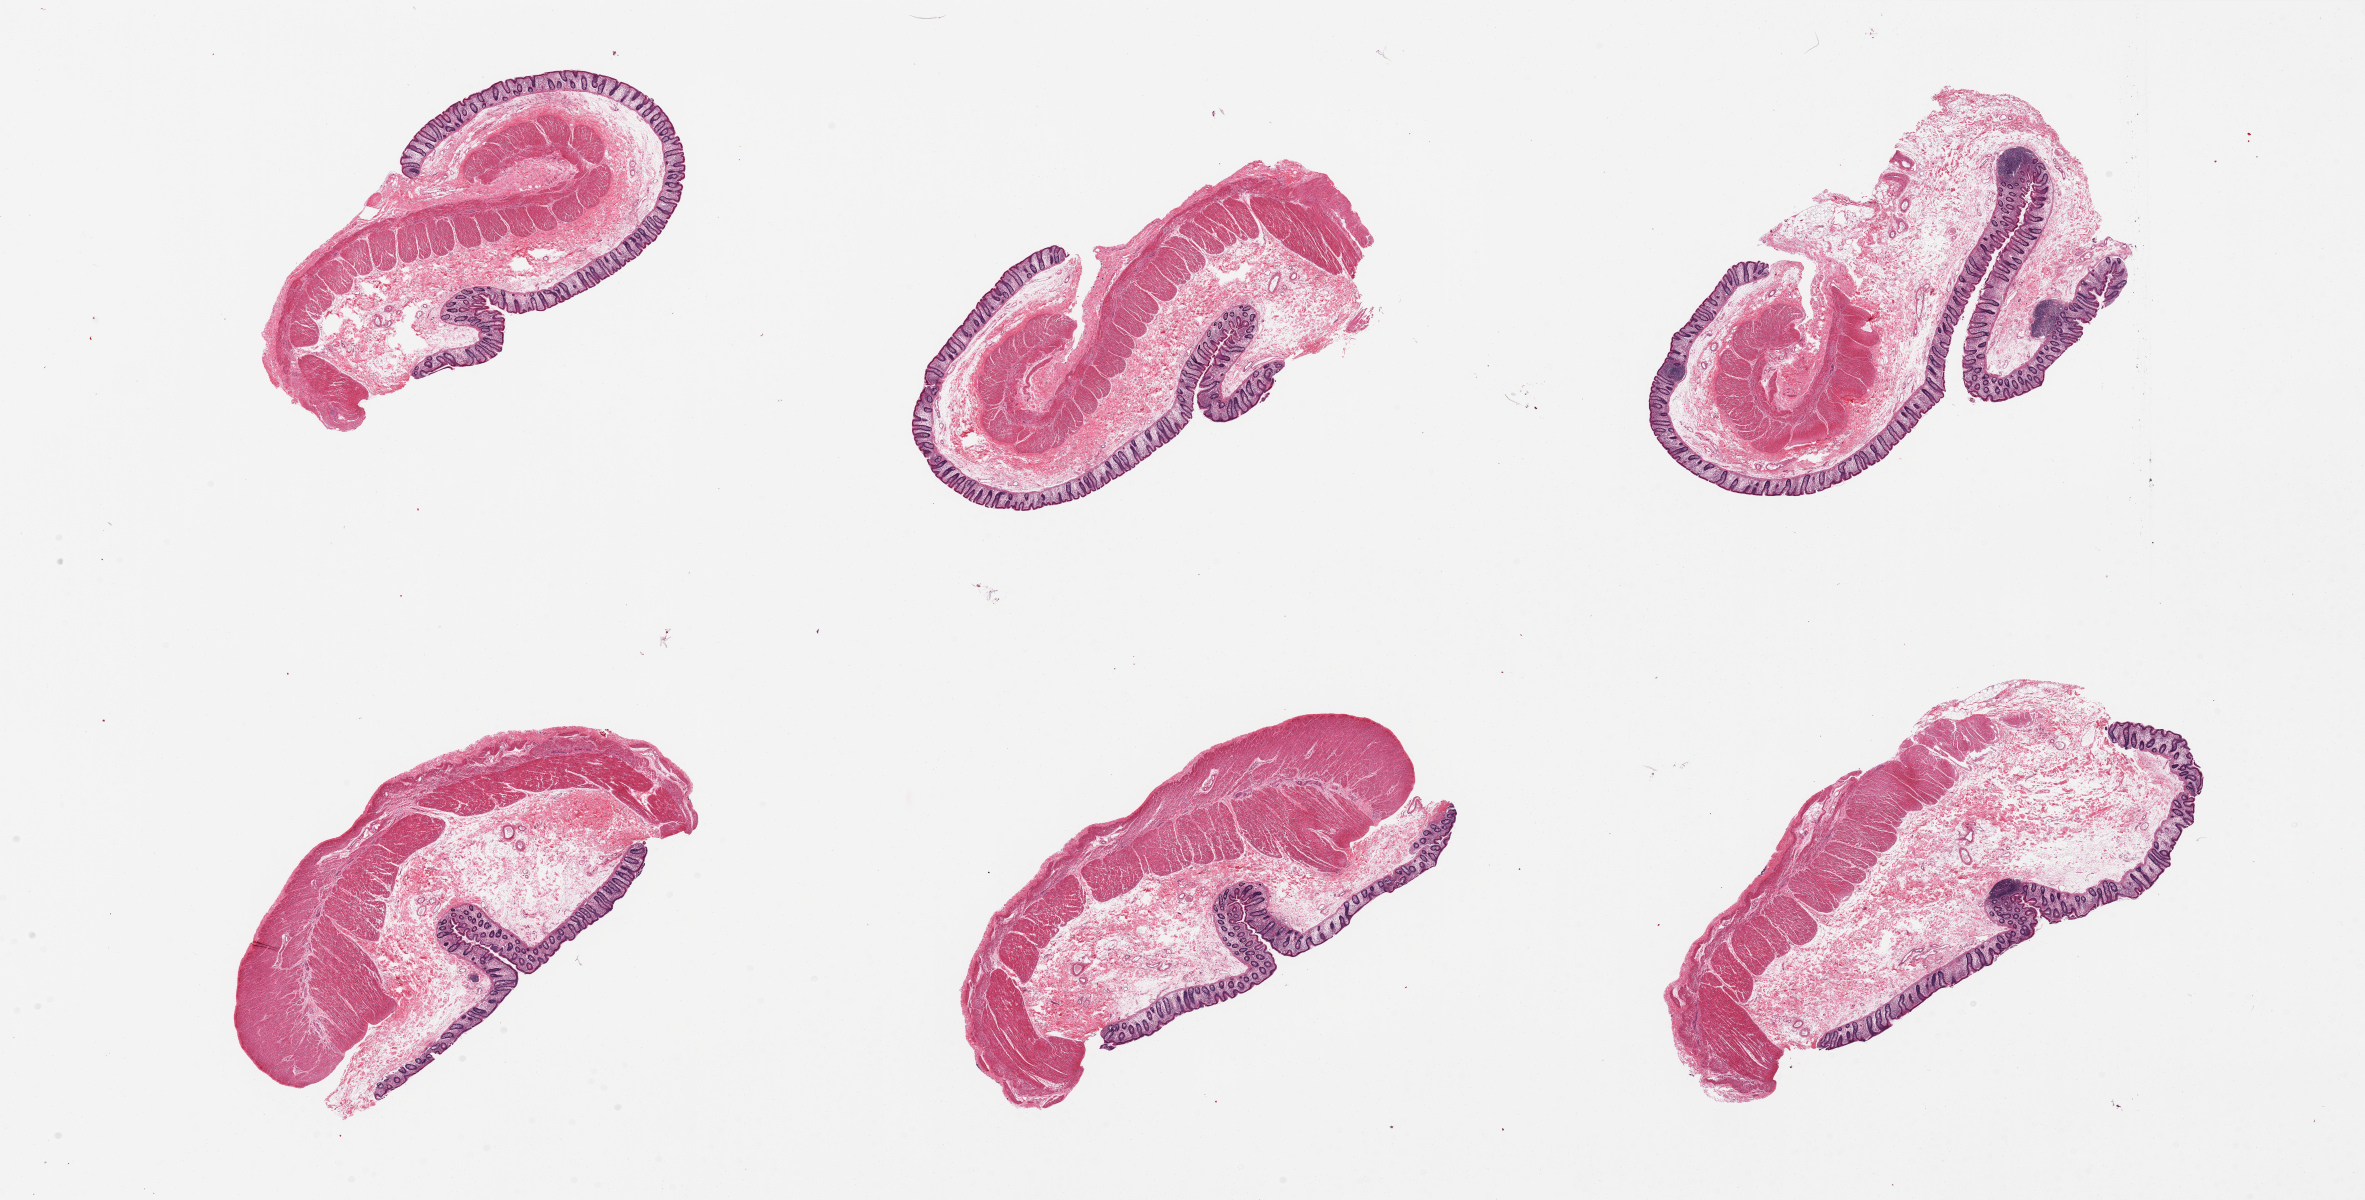
Whole-slide image, hematoxylin and eosin (H&E) stain, brightfield, shown as a low-resolution overview of the whole scanned area (about 37.4 x 19.0 mm); PAXgene-fixed paraffin-embedded (PFPE) section; target tissue: transverse colon; donor tissue sample.
Review note (as recorded): 6 pieces; submucosal edema, full thickness.